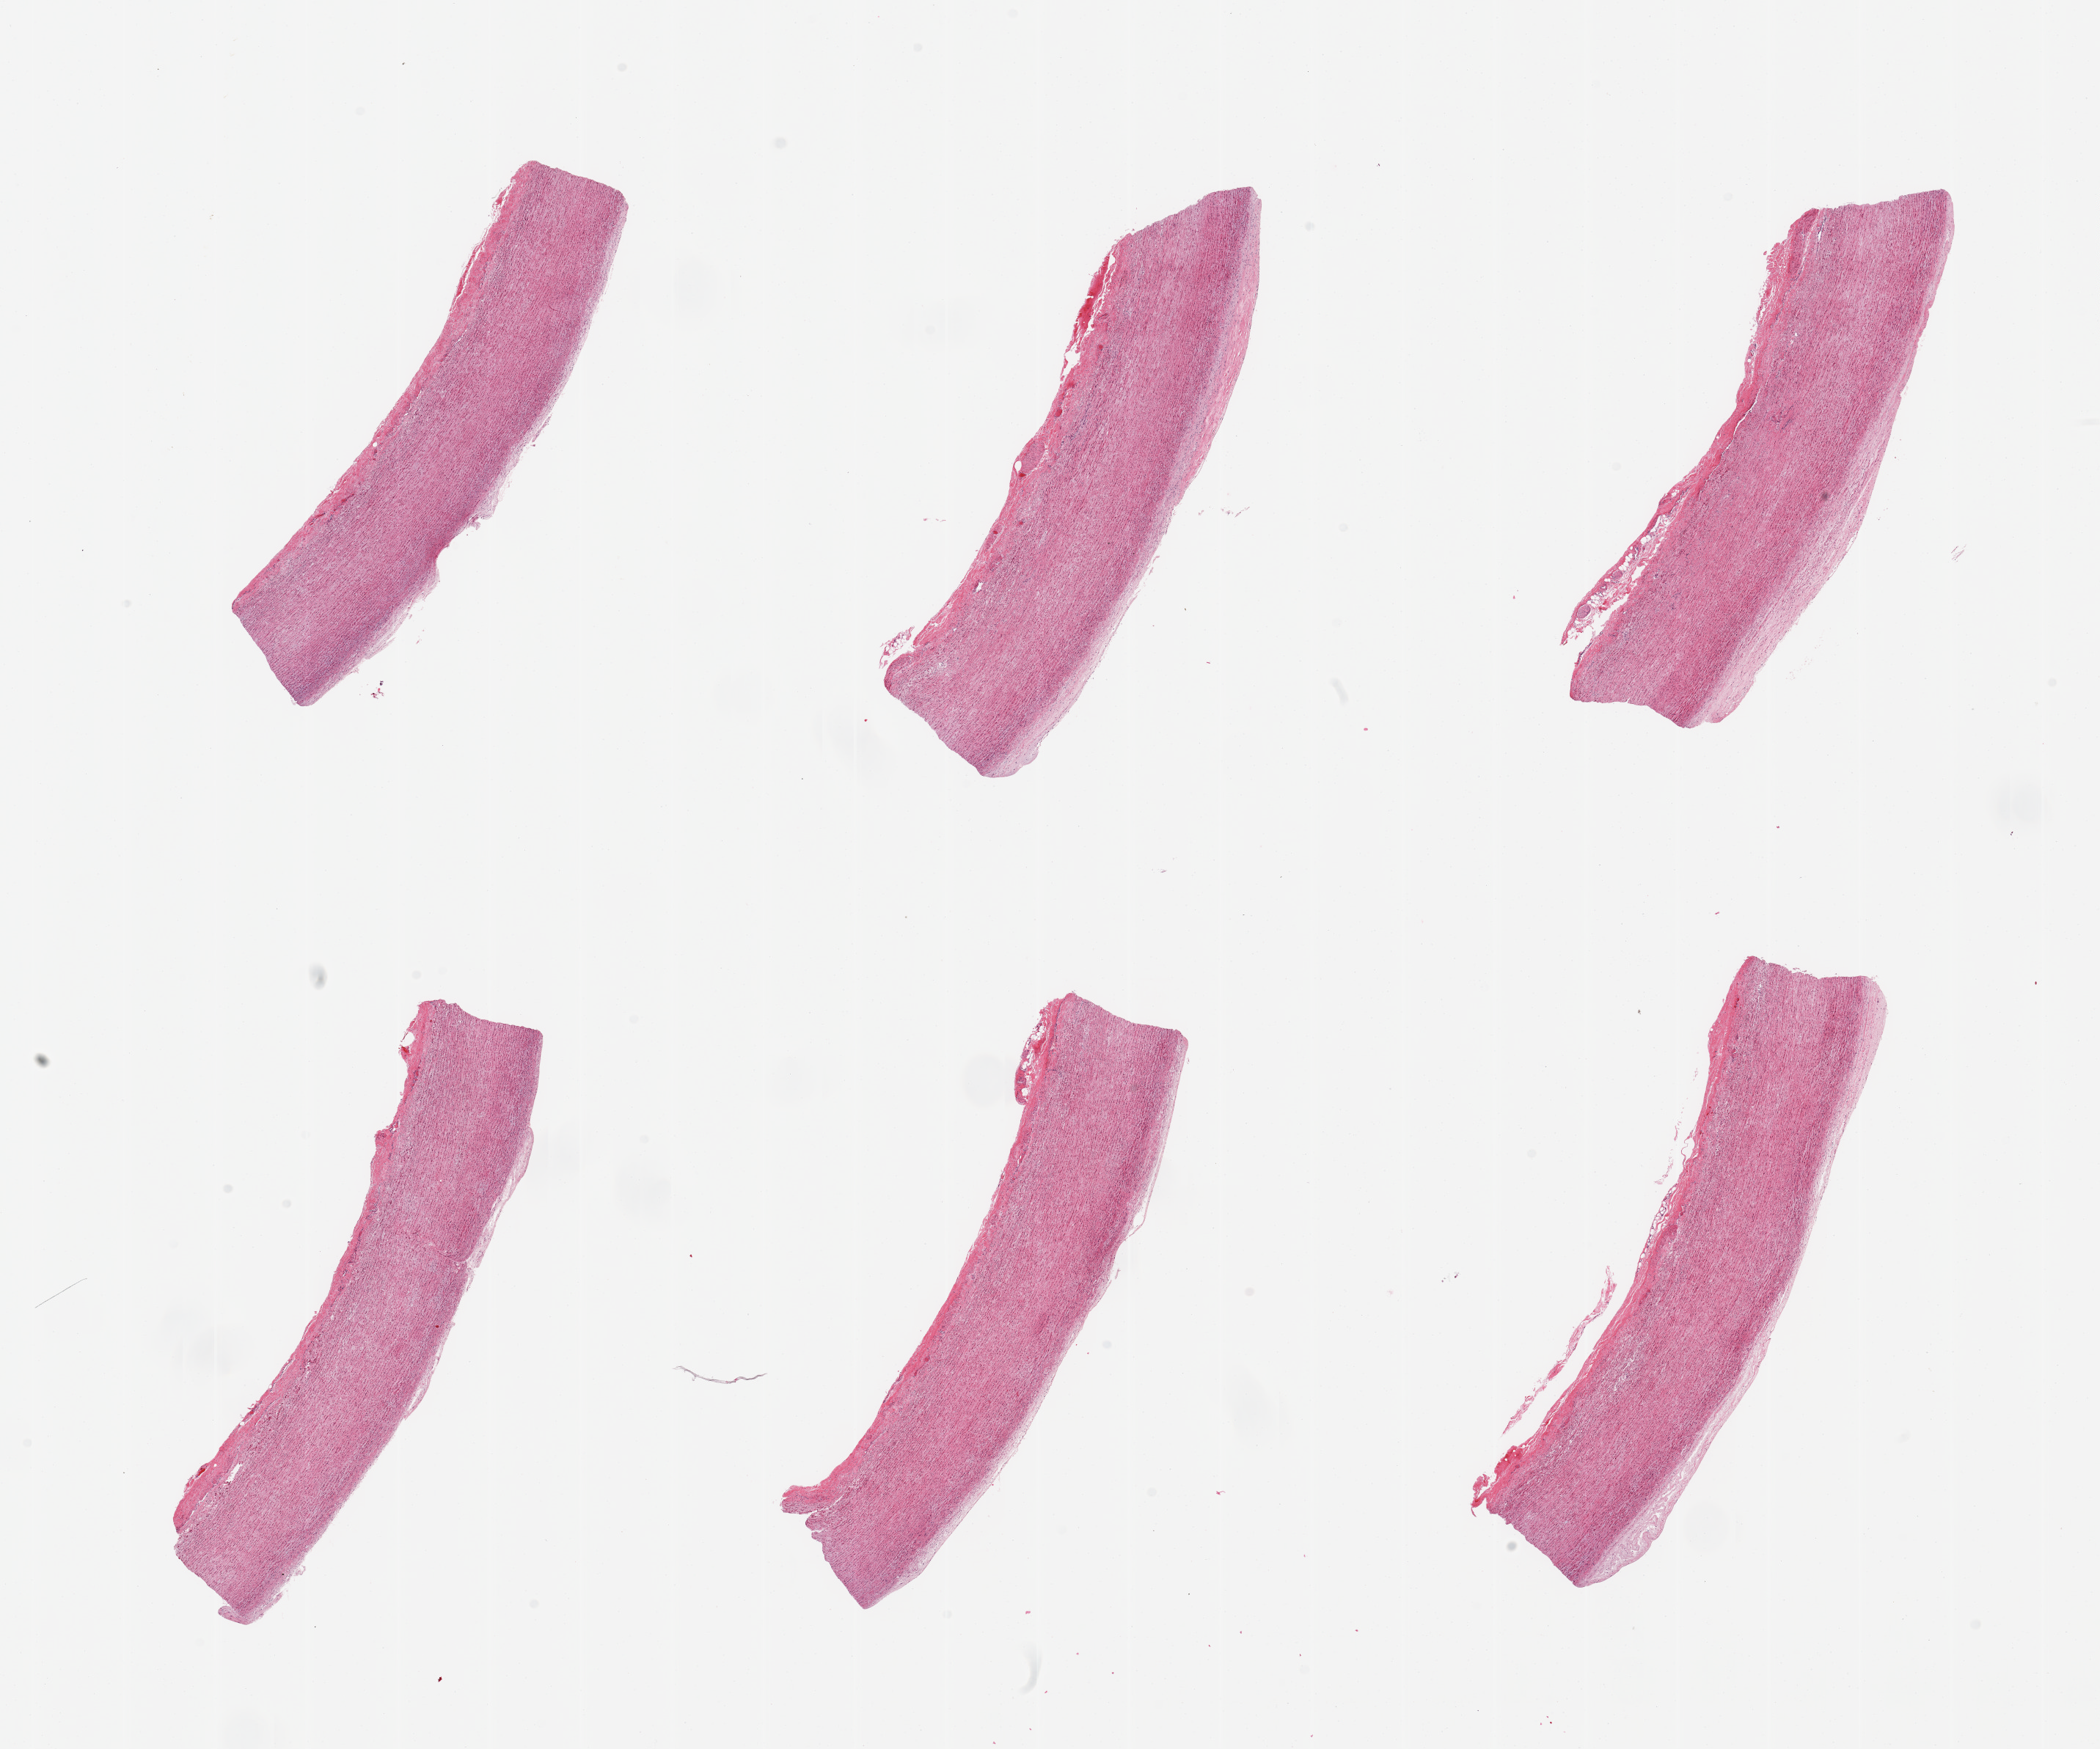
Digitized haematoxylin and eosin-stained section — low-resolution overview of the scanned area, about 22.6 x 18.9 mm, PAXgene-fixed paraffin-embedded (PFPE) section, section of aorta (target tissue), tissue donor sample. Donor: male.
Review note (as recorded): 6 pieces, atherosis up to ~0.3mm.